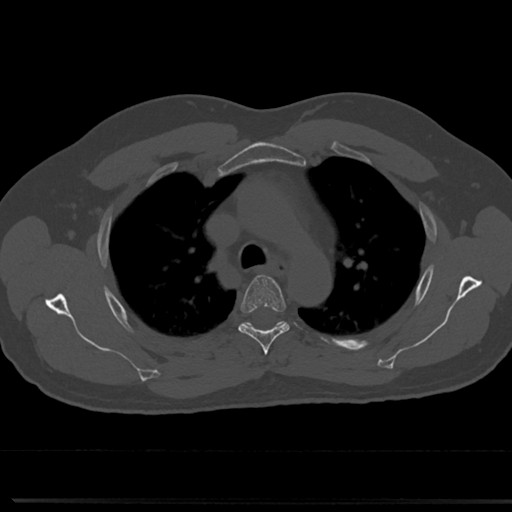
CT including the spine, one axial slice. Position 539 of 817 along the scan axis. Reconstruction kernel Br40s/3. 120 kVp. Bone window (W 1800 / L 400 HU). 0.5 mm slice thickness. 512 × 512 image matrix. Male patient, age 61 years. From the clinical record (not read from this slice): primary cancer: prostate.
Annotated regions visible in this slice (semi-automatically segmented with operator editing):
- T4 vertebra: bounding box <237,275,291,353> (left, top, right, bottom; pixels)
- T5 vertebra: <246,322,283,326>